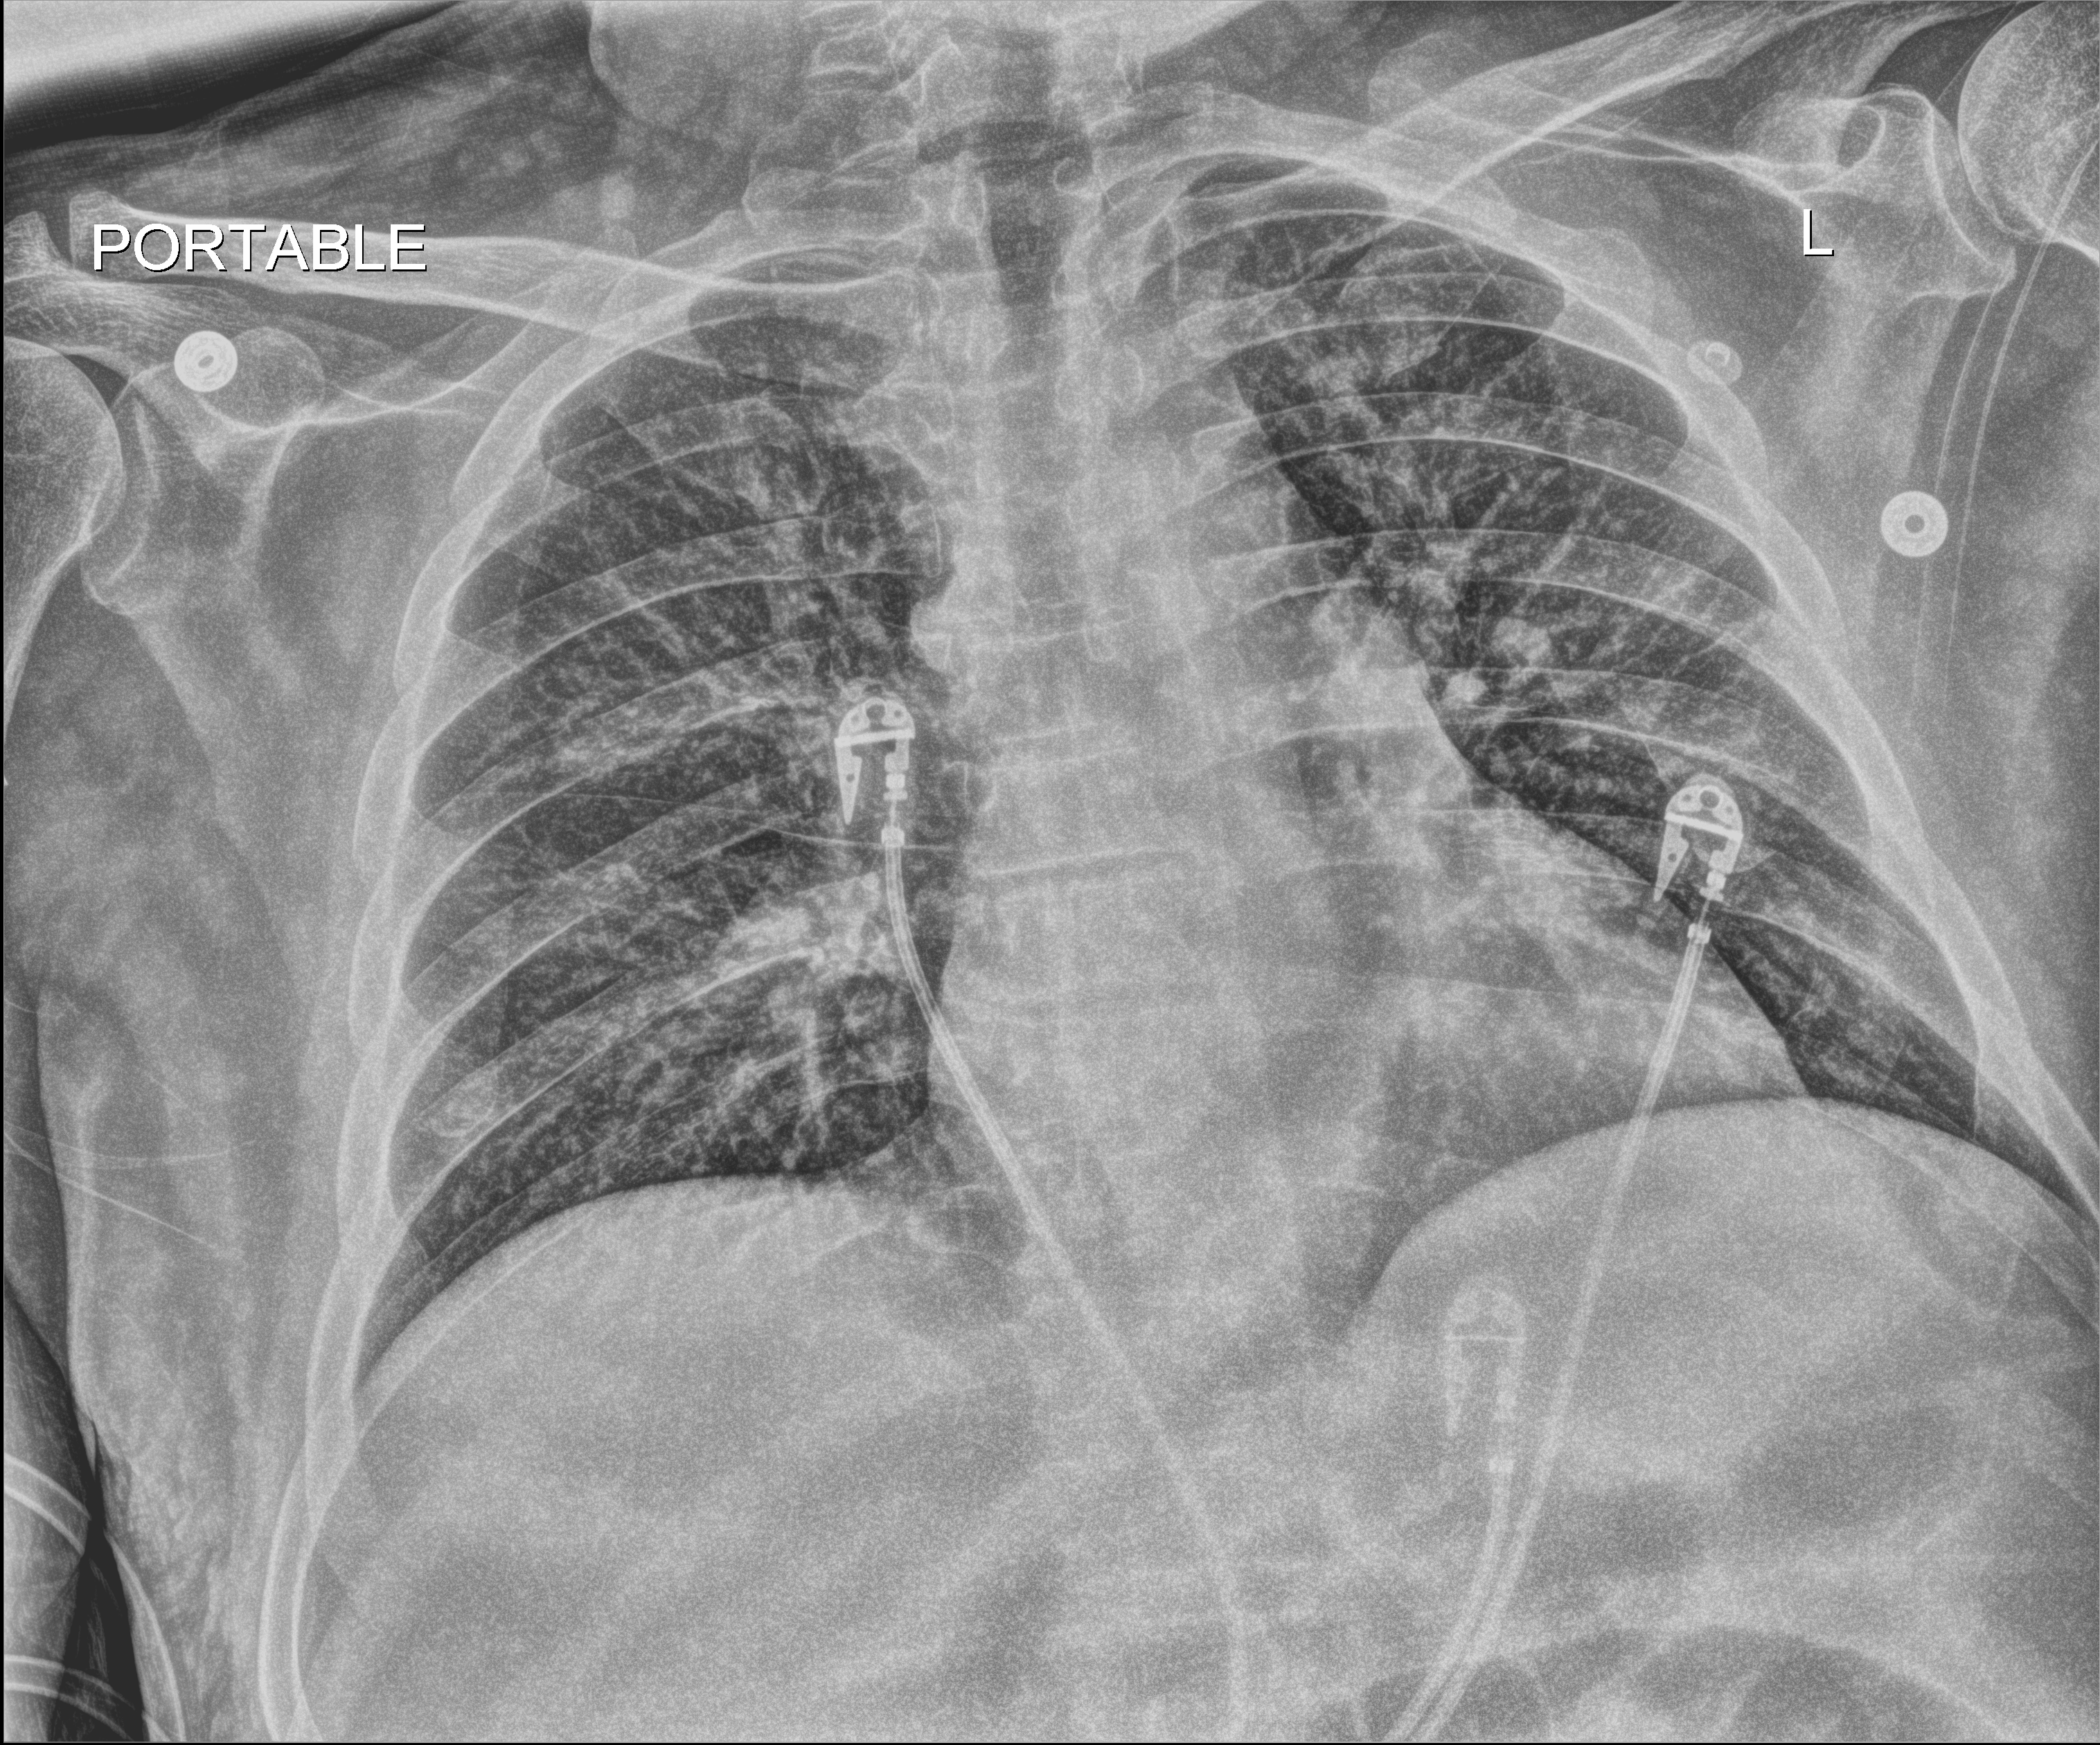
Bedside chest radiograph (digital radiography). Male patient hospitalised with COVID-19, age 18–59 years.
Admission-level facts for this patient (not findings on this image; timing relative to this image not recorded):
- admitted to intensive care during this hospital stay: yes
- mechanically ventilated during this hospital stay: no